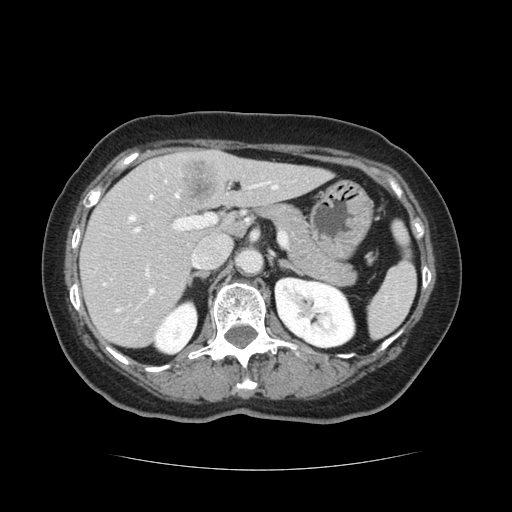
Contrast-enhanced abdominal CT, one axial slice; slice 71 of 128 in the series (ordered by position); 120 kVp; intravenous contrast given; soft-tissue window (W 400 / L 40 HU); 2.5 mm slice thickness; 512 × 512 image matrix, field of view 366 × 366 mm. Female patient, age 67 years. From the clinical record (not read from this slice): diagnosis: colorectal cancer liver metastases, imaged before liver resection; multiple liver metastases: yes; largest metastasis: 3 cm.
Annotated regions visible in this slice (expert manual segmentation):
- hepatic veins: bounding box <104,186,278,311> (left, top, right, bottom; pixels)
- liver: <81,149,327,347>
- planned liver remnant (the part of the liver to remain after resection): <81,161,327,347>
- portal vein (with intrahepatic branches): <133,180,272,296>
- liver metastasis: <177,160,223,201>